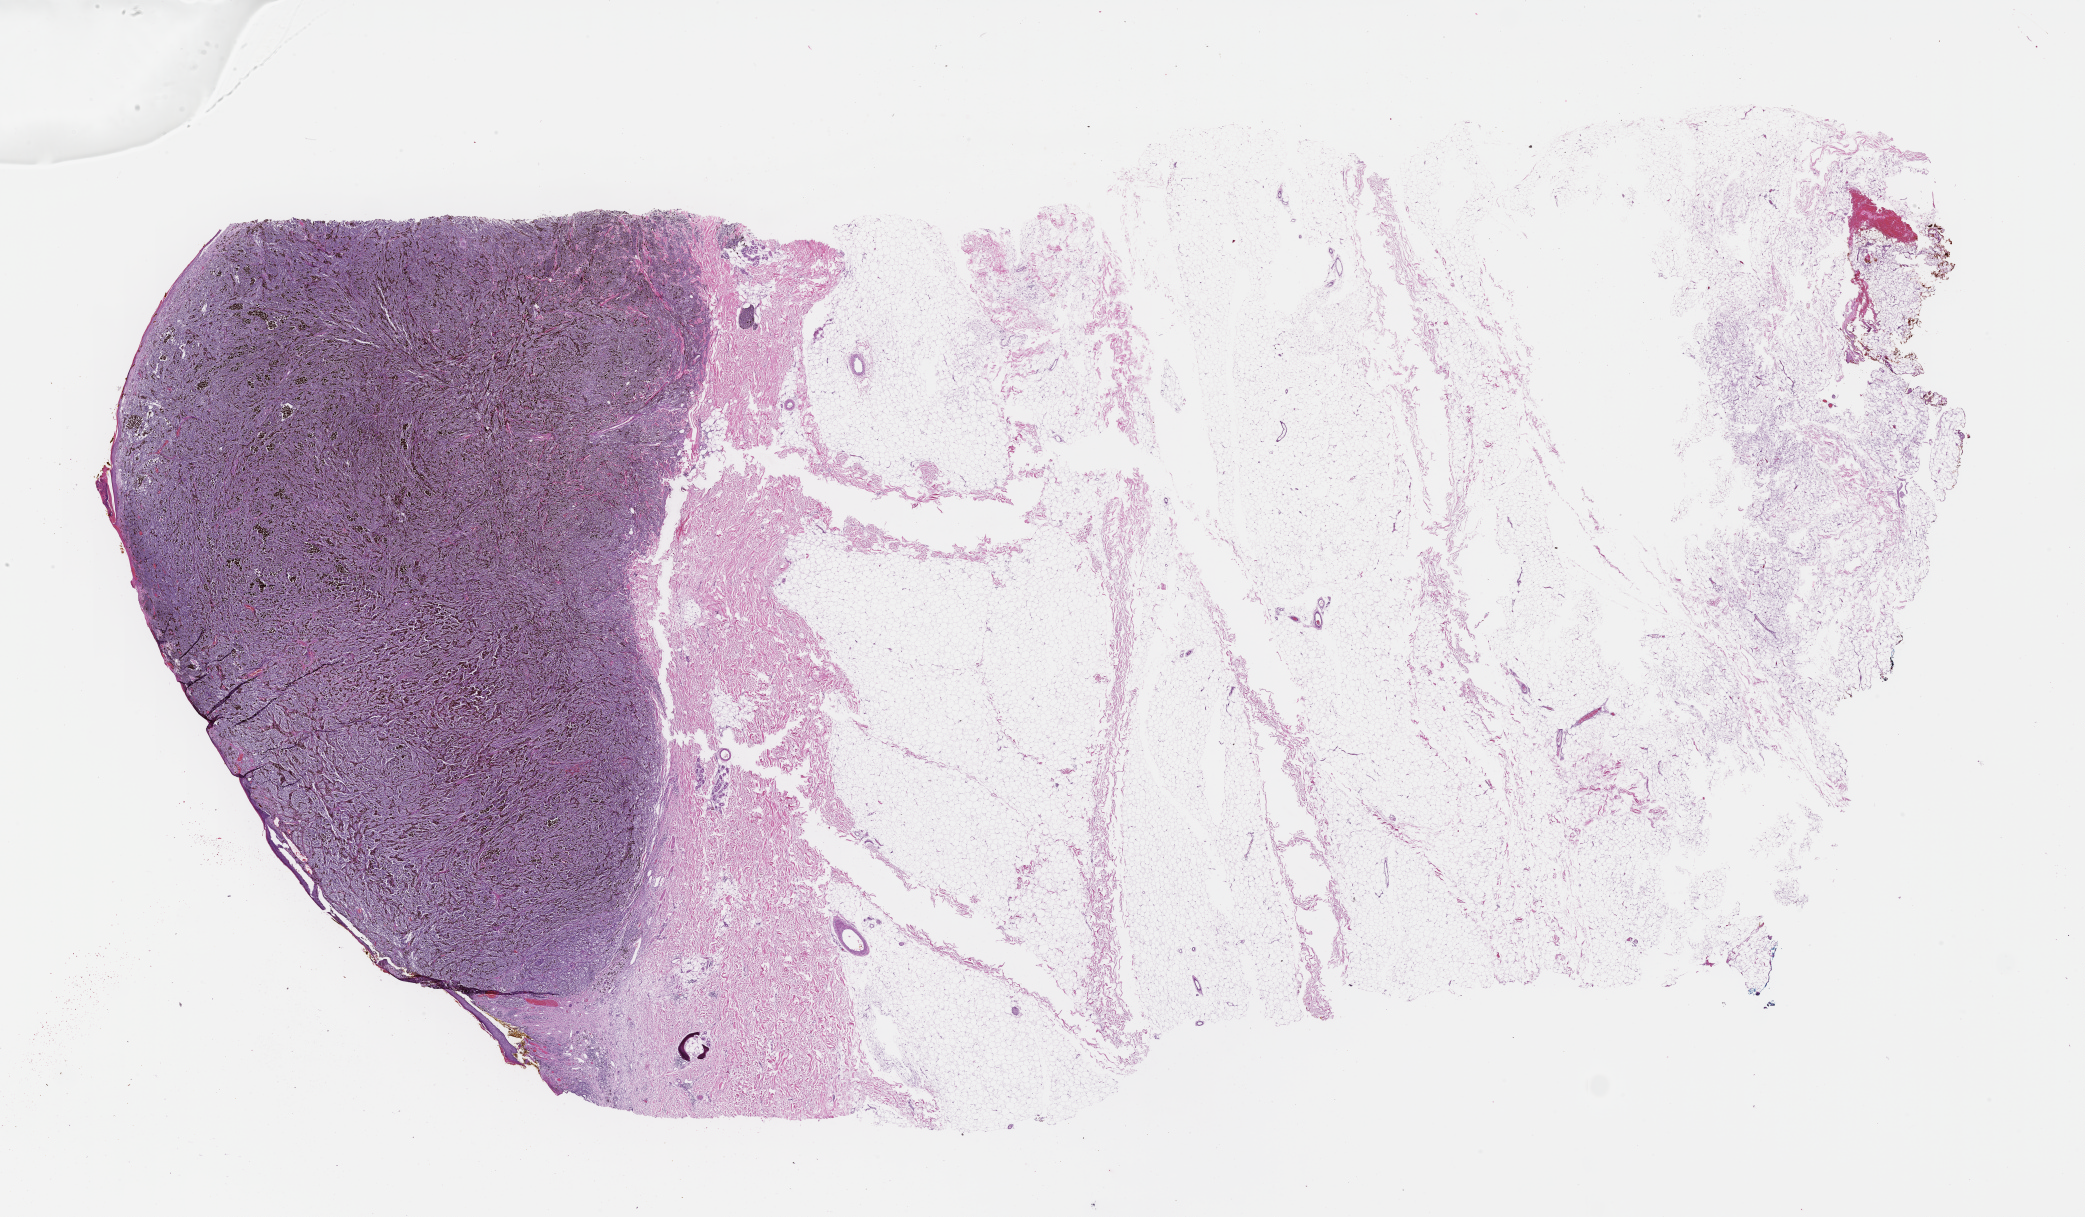
Haematoxylin and eosin whole-slide image, a low-resolution overview of the entire scanned area, about 33.7 x 19.7 mm, formalin-fixed paraffin-embedded section, site: skin. Male patient.
This section: primary tumour tissue. Diagnosis: Melanoma.